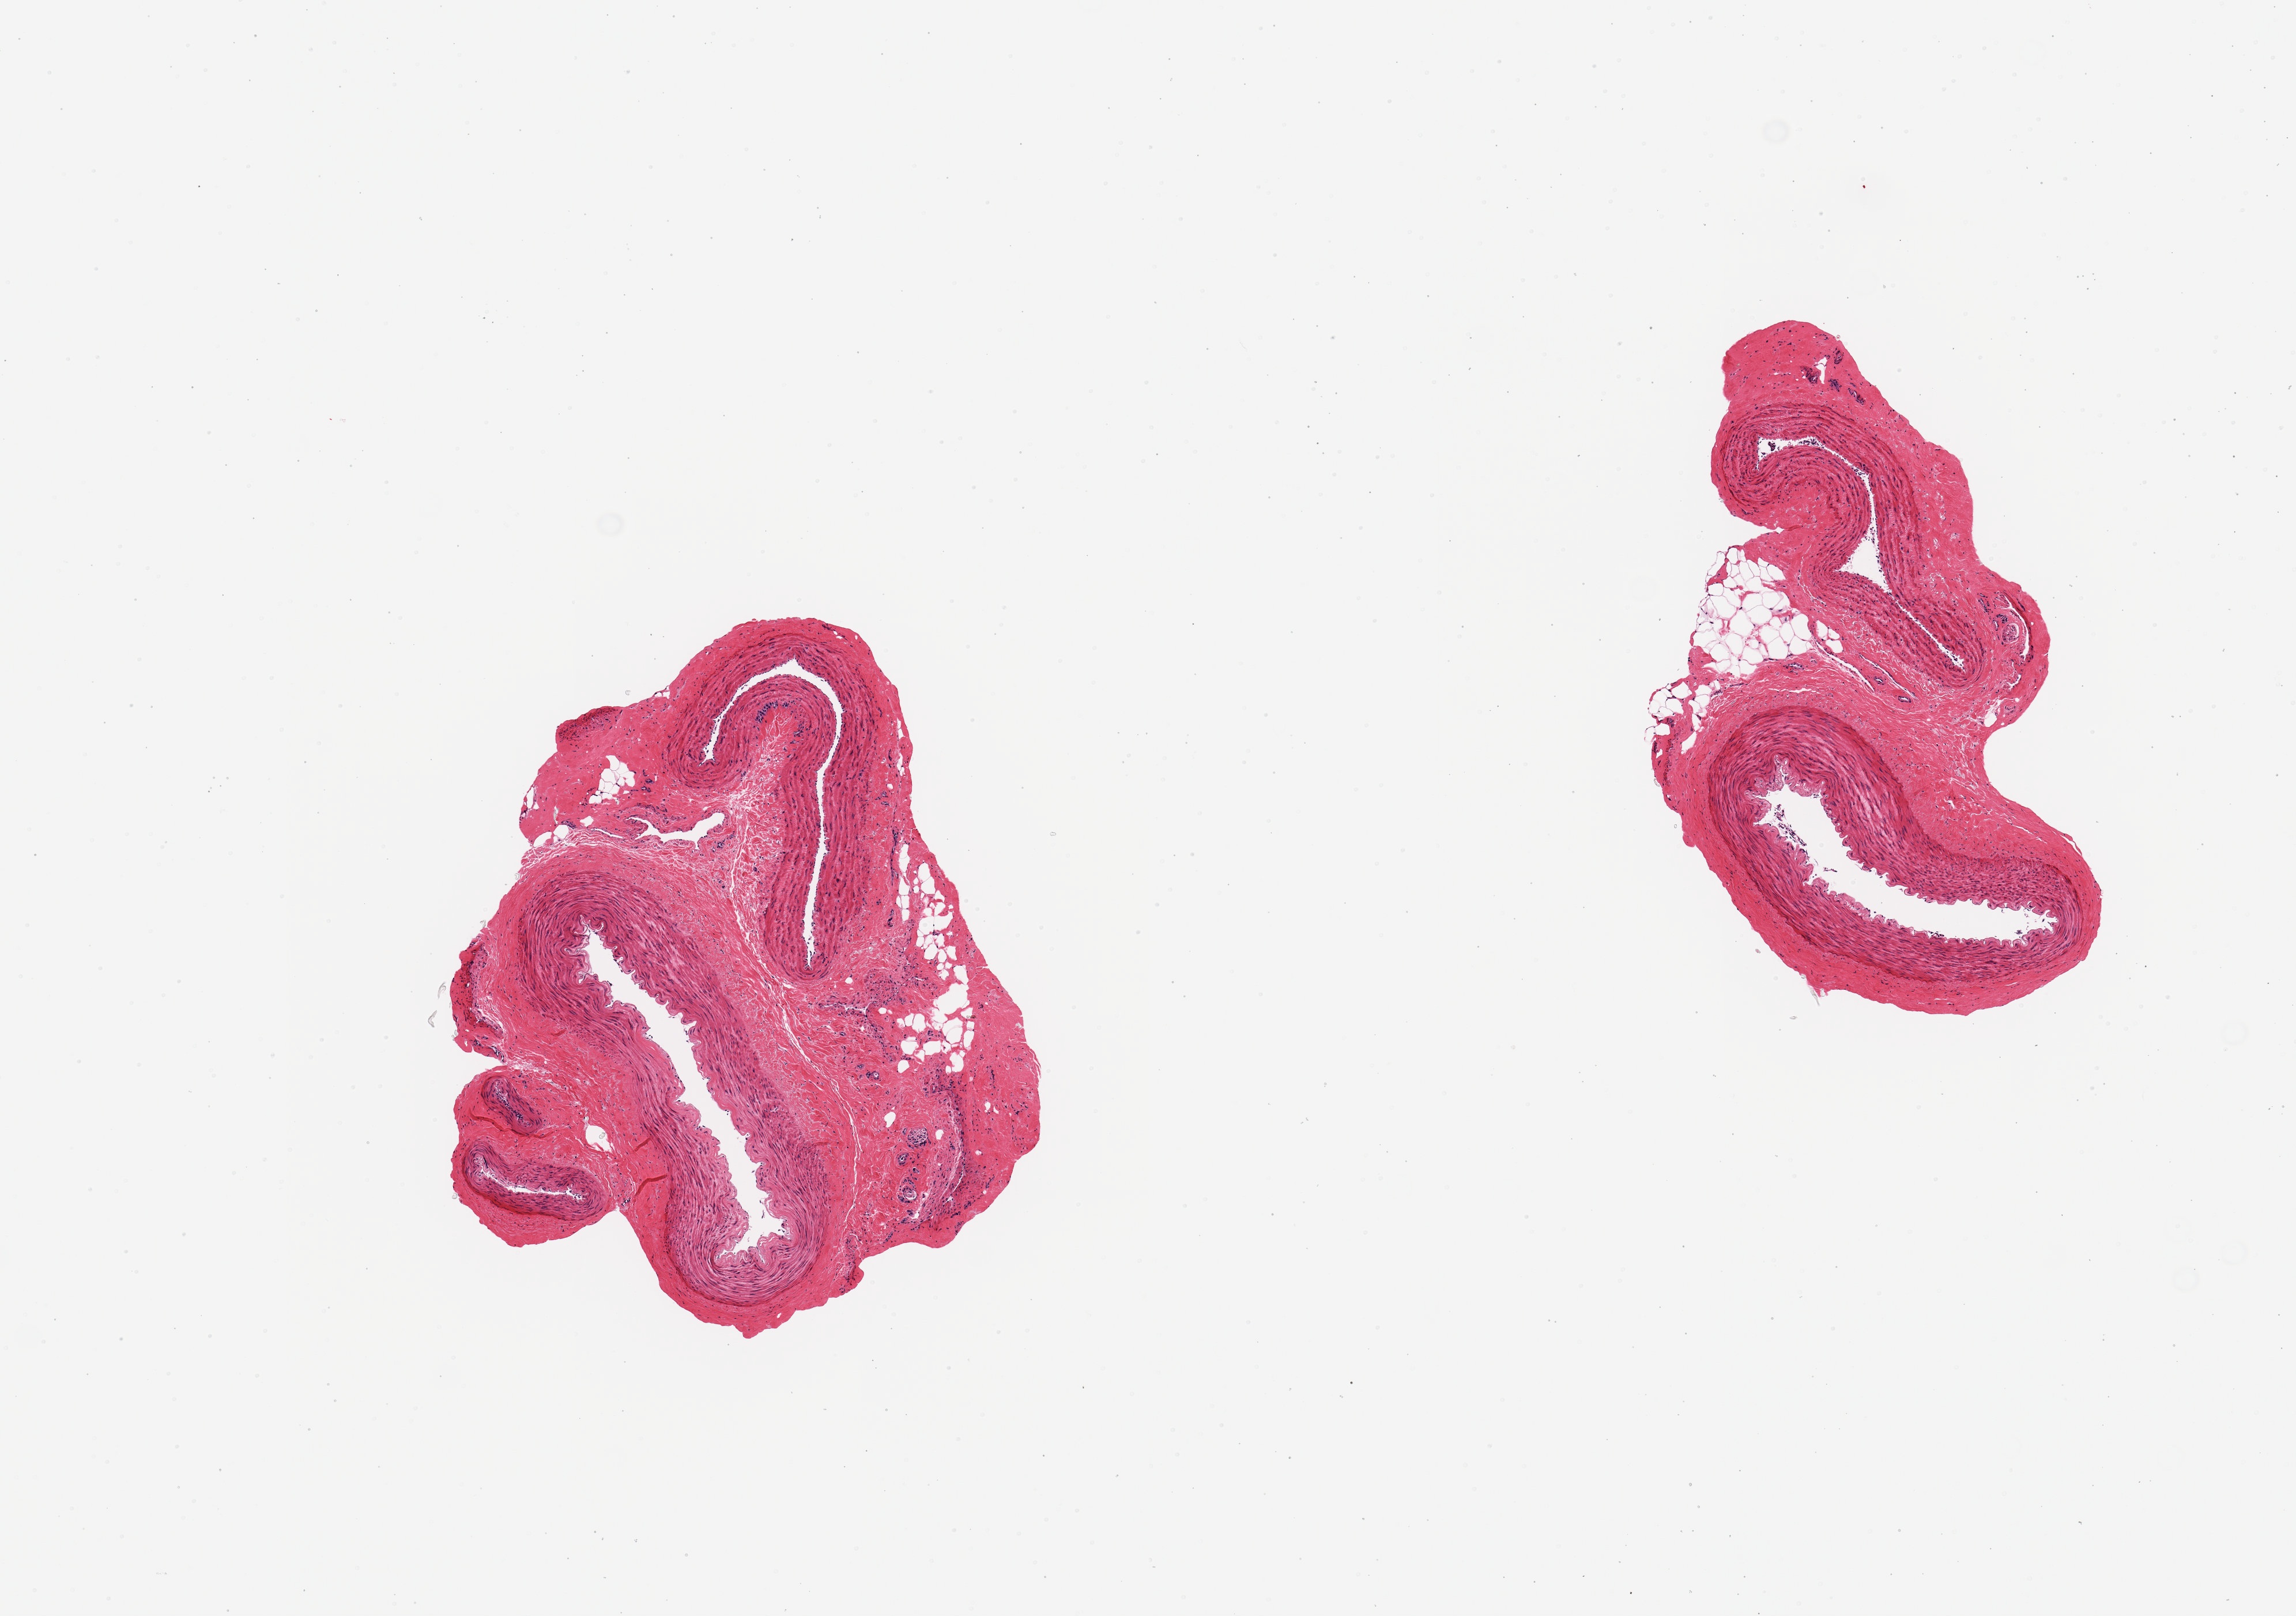
Haematoxylin and eosin whole-slide image, whole scanned area (about 7.9 x 5.5 mm, from a 20x scan) shown as a low-resolution overview. PAXgene-fixed, paraffin-embedded tissue. Target tissue: tibial artery. Donor tissue sample.
Reviewer comment on this tissue sample: 2 pieces; cross sections of vessels with attached adventitia and trace of external fat.